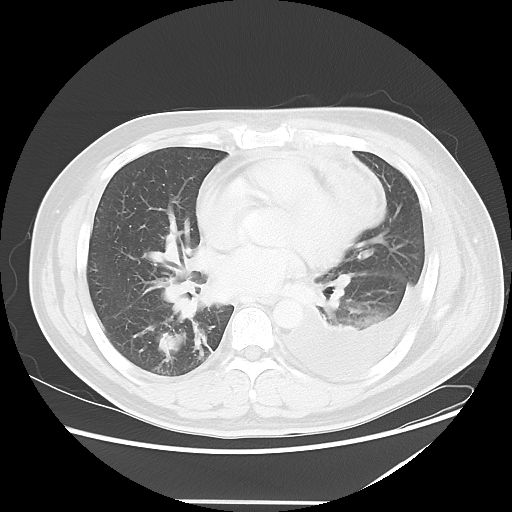
Chest CT, one axial slice. Slice 23 of 52 in the series (ordered by position). Reconstruction kernel LUNG. Lung window (W 1500 / L -600 HU). 5 mm slice thickness. 512 × 512 image matrix, field of view 405 × 405 mm. Male patient, age 42 years. From the clinical record (not read from this slice): clinical TNM (as recorded): T2 N1 M1.
Structures marked on this image (bounding box drawn by a radiologist):
- lung tumour (recorded histology: adenocarcinoma): bounding box [x1, y1, x2, y2] px = [151, 330, 197, 360]